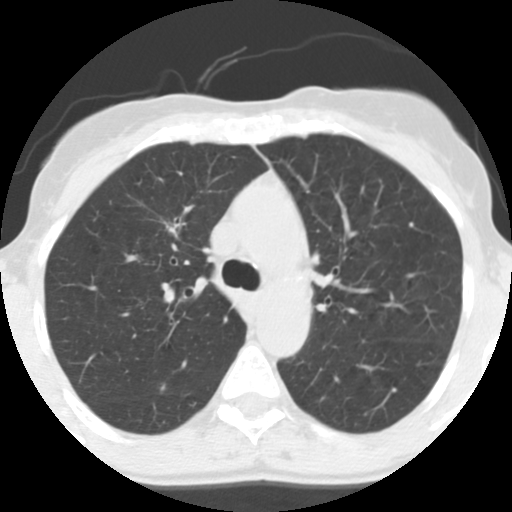
Chest CT (low-dose screening protocol), one axial image, first (baseline) screen, lung window (W 1500 / L -600 HU), 140 kVp, slice 46 of 130 in the series, 512 × 512 image matrix, field of view 277 × 277 mm. Female, age 56 years at enrolment. Former smoker at enrolment.
Expert reader's lesion annotation, bounding box [x1, y1, x2, y2] px = [151, 208, 195, 248]. The exam's reader record, not a measurement of the box and not confirmed to be the same lesion: non-calcified nodule or mass ≥4 mm, right upper lobe, 12 × 9 mm, spiculated (stellate) margins, soft tissue attenuation. Lung cancer was diagnosed 779 days after this screen (after the third annual screen): adenocarcinoma, NOS, right upper lobe, moderately differentiated (G2), stage IA (AJCC 6th edition), 19 mm at pathology.